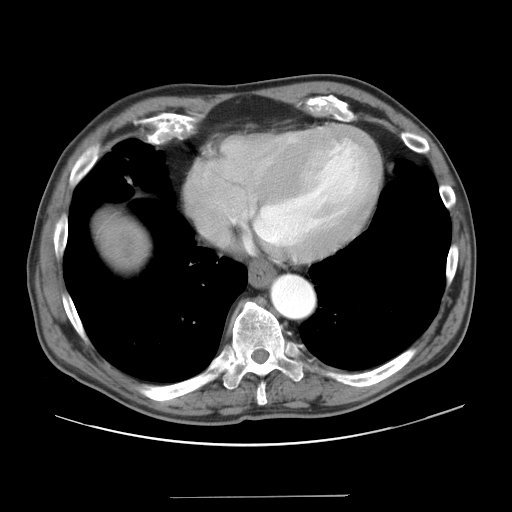
Contrast-enhanced abdominal CT, one axial slice. Slice 40 of 41 in the series (ordered by position). Reconstruction kernel STANDARD. 120 kVp. Intravenous contrast given. Soft-tissue window (W 400 / L 40 HU). 5 mm slice thickness. 512 × 512 image matrix, field of view 420 × 420 mm. Male patient, age 75 years. From the clinical record (not read from this slice): diagnosis: colorectal cancer liver metastases, imaged before liver resection; multiple liver metastases: no; largest metastasis: 5.2 cm.
Structures marked on this image (manually delineated by an expert):
- liver: bounding box [x1, y1, x2, y2] px = [103, 220, 146, 270]
- liver metastasis: [123, 249, 133, 260]